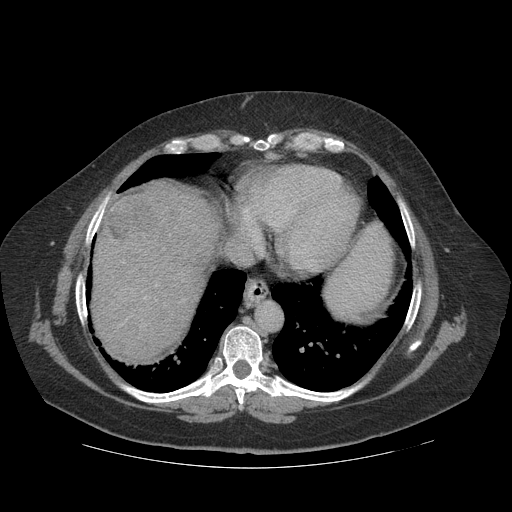
Contrast-enhanced abdominal CT (liver protocol), one axial slice. Reconstruction kernel STANDARD. 140 kVp. Soft-tissue window (W 400 / L 40 HU). 512 × 512 image matrix. Case-level facts recorded for this patient, not image findings: diagnosis: hepatocellular carcinoma (patient treated with transarterial chemoembolisation; whether this scan precedes or follows treatment is not stated here); TNM stage (as recorded): Stage-IIIA; Child-Pugh class: A; tumour nodularity: multinodular.
Outlined on this slice (semi-automatic segmentation, software-assisted and operator-edited):
- abdominal aorta: bounding box [x1, y1, x2, y2] px = [257, 301, 282, 332]
- liver parenchyma outside the tumour (the mass and vessels are separate outlines, so this box may not span the whole liver): [92, 180, 219, 360]
- mass: [102, 189, 160, 244]
- liver vessels: [144, 297, 147, 299]